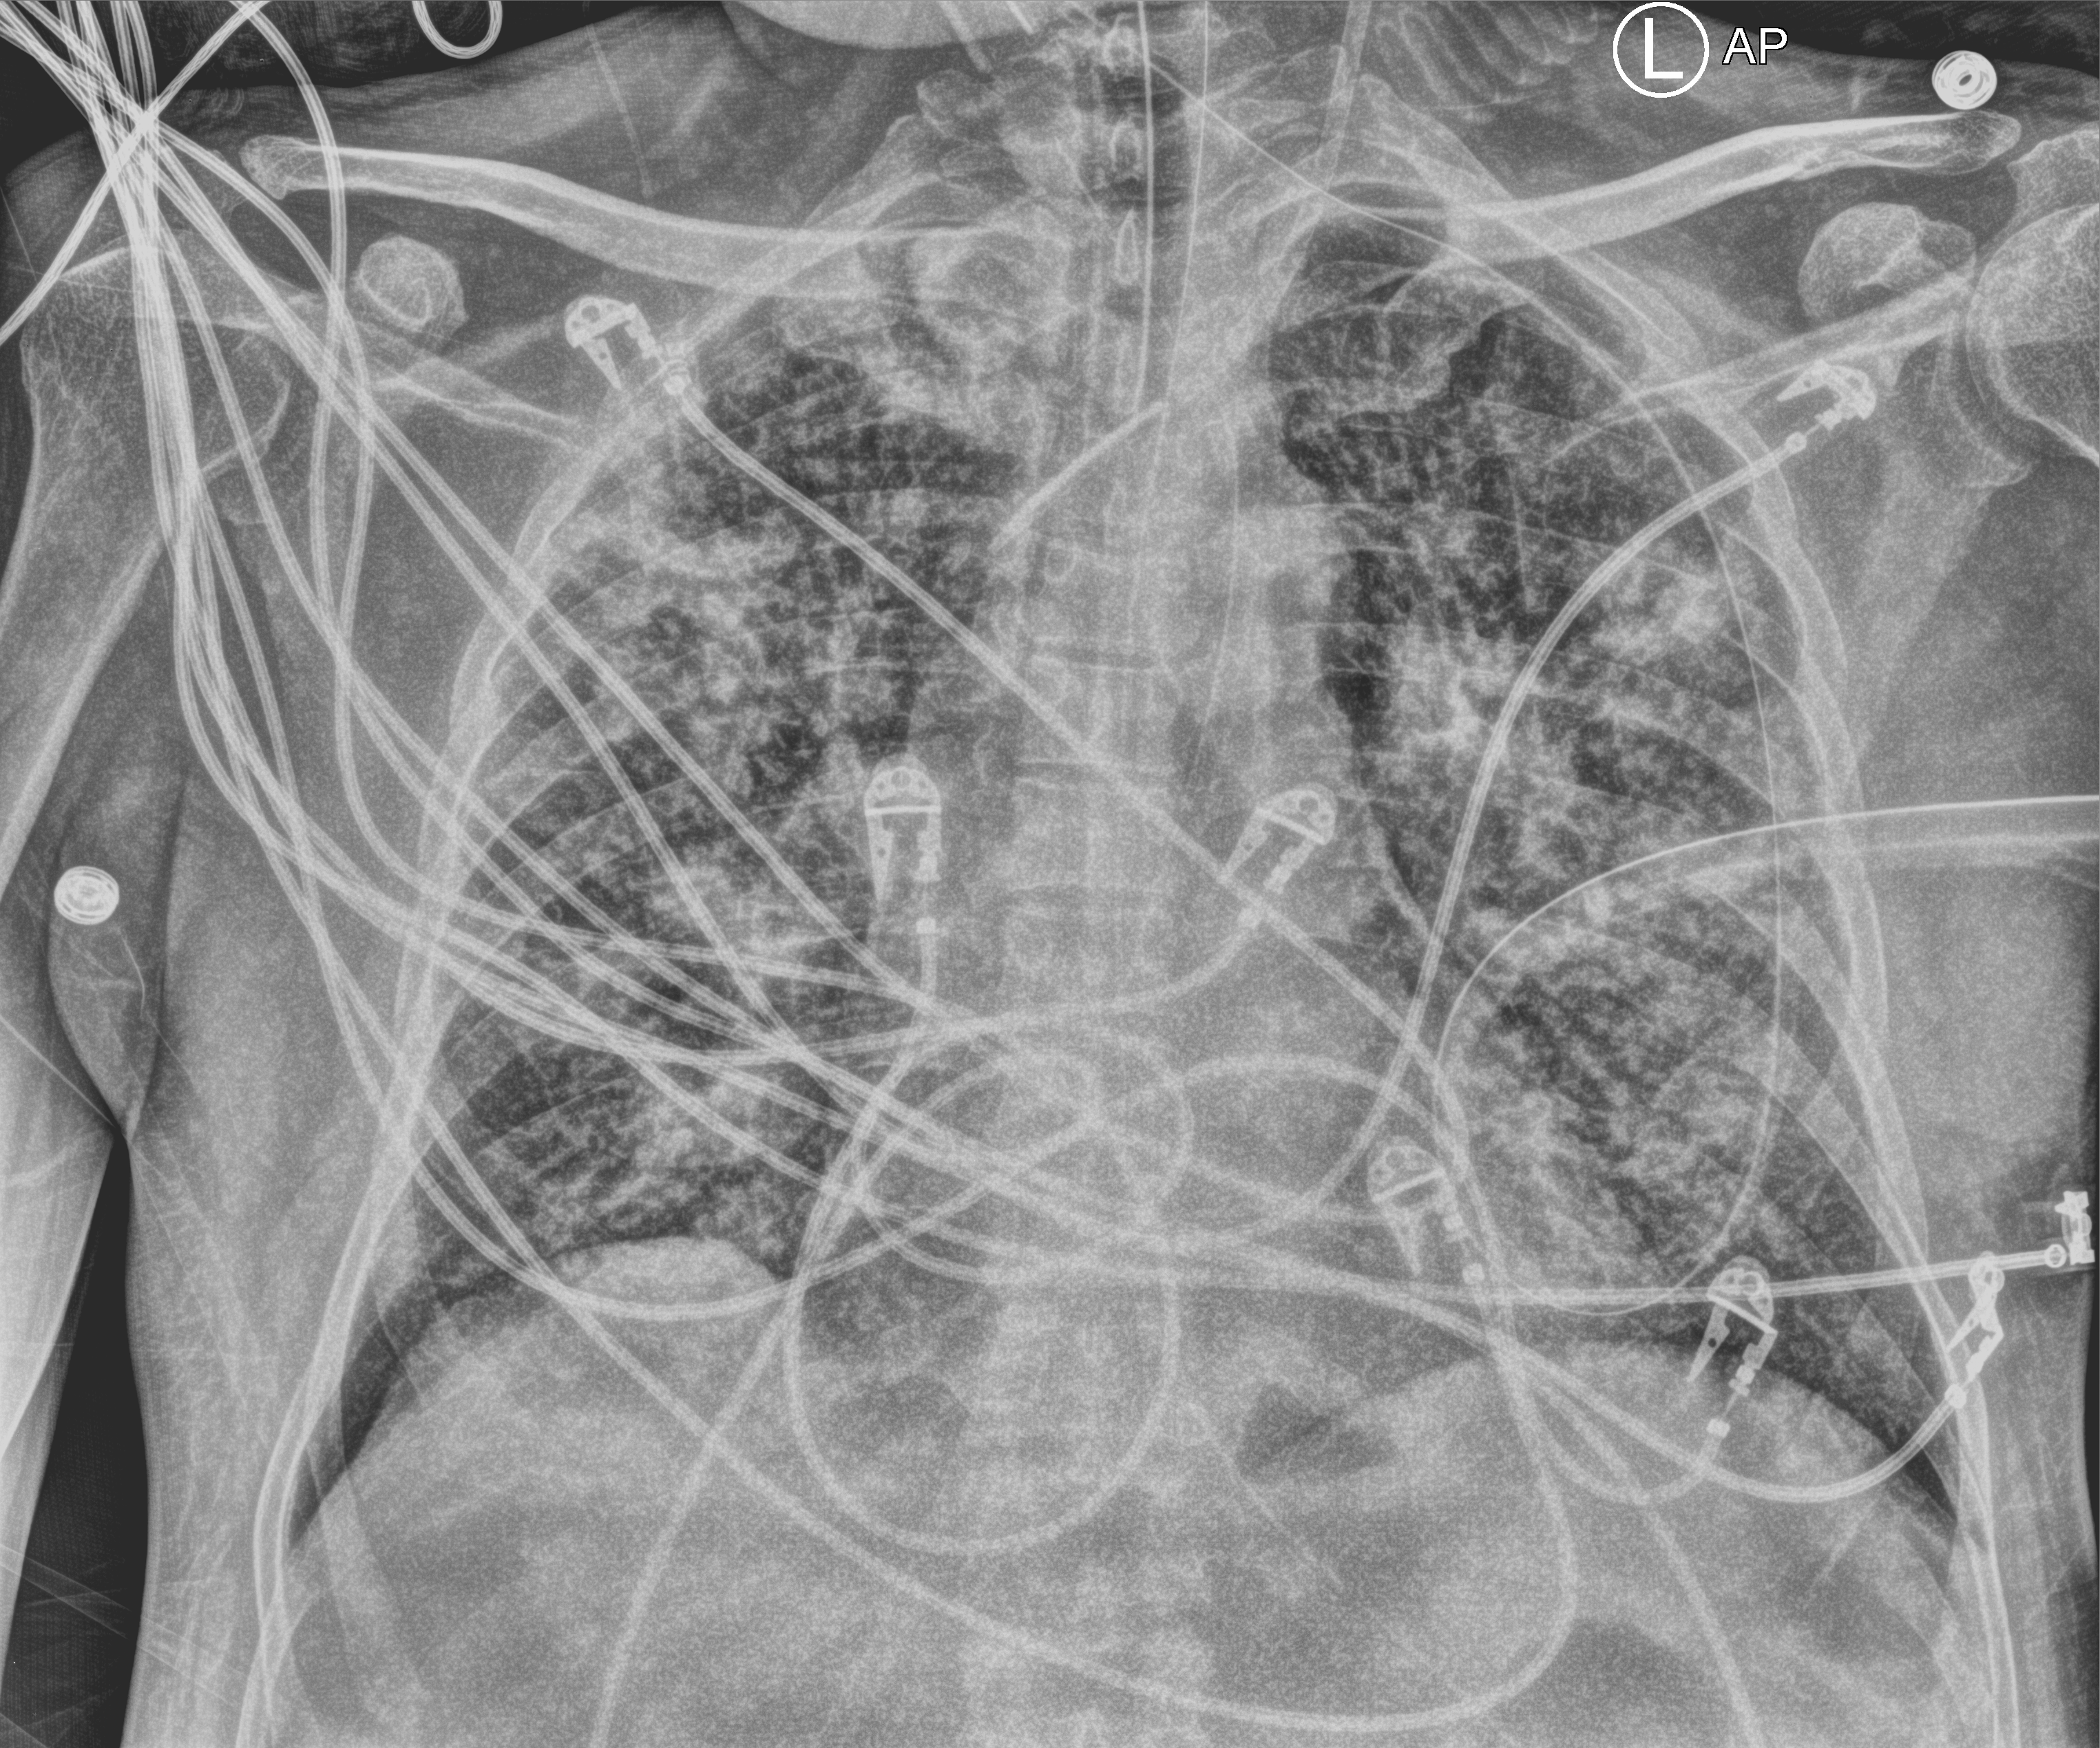
Chest X-ray (portable), anteroposterior (AP) projection. Male patient hospitalised with COVID-19, age 60–74 years.
Admission-level facts for this patient (not findings on this image; timing relative to this image not recorded):
- admitted to intensive care during this hospital stay: yes